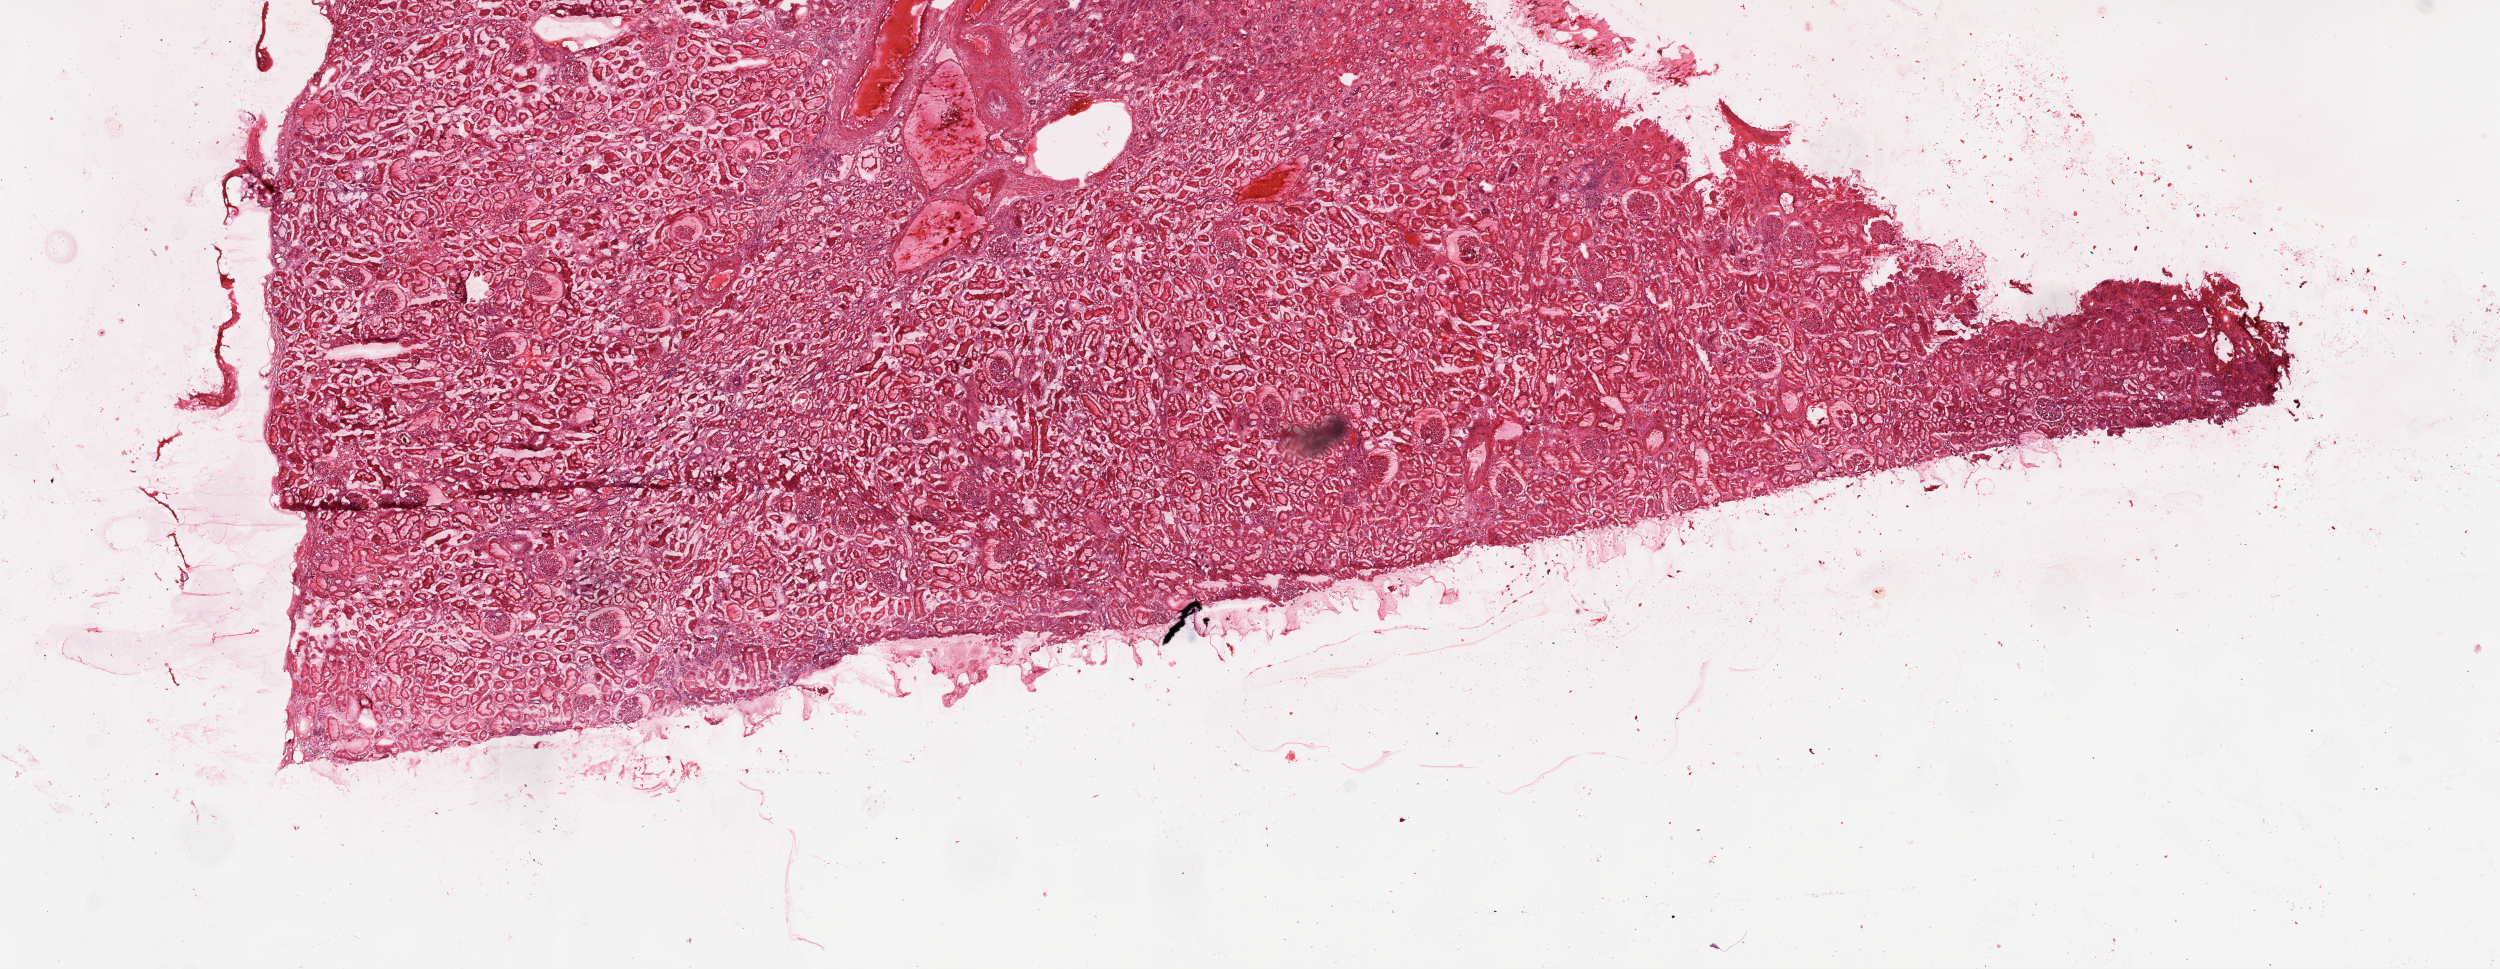
Digitized Hematoxylin and eosin (H&E) stained tissue section (whole slide) — shown as a low-resolution overview of the whole scanned area (about 20.1 x 7.8 mm, slide scanned at 20x), frozen section from the top of the tissue portion, solid tissue normal (non-tumour tissue) sample from the kidney. Female patient; age at initial diagnosis 69 years.
This section: solid tissue normal sample (biorepository sample class). Patient diagnosis: Clear cell adenocarcinoma, NOS.